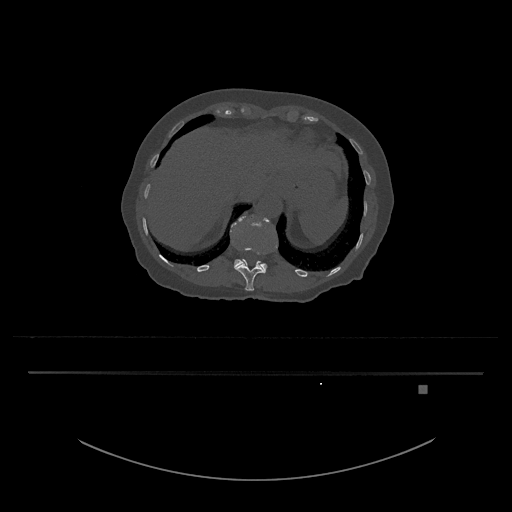
CT including the spine, one axial slice; position 591 of 797 along the scan axis; reconstruction kernel Br40s/3; 120 kVp; bone window (W 1800 / L 400 HU); 0.5 mm slice thickness; 512 × 512 image matrix, field of view 500 × 500 mm. Female patient, age 57 years. From the clinical record (not read from this slice): primary cancer: cervical.
Outlined on this slice (semi-automatically segmented with operator editing):
- L1 vertebra: bounding box <231,215,270,271> (left, top, right, bottom; pixels)
- T12 vertebra: <235,248,266,291>